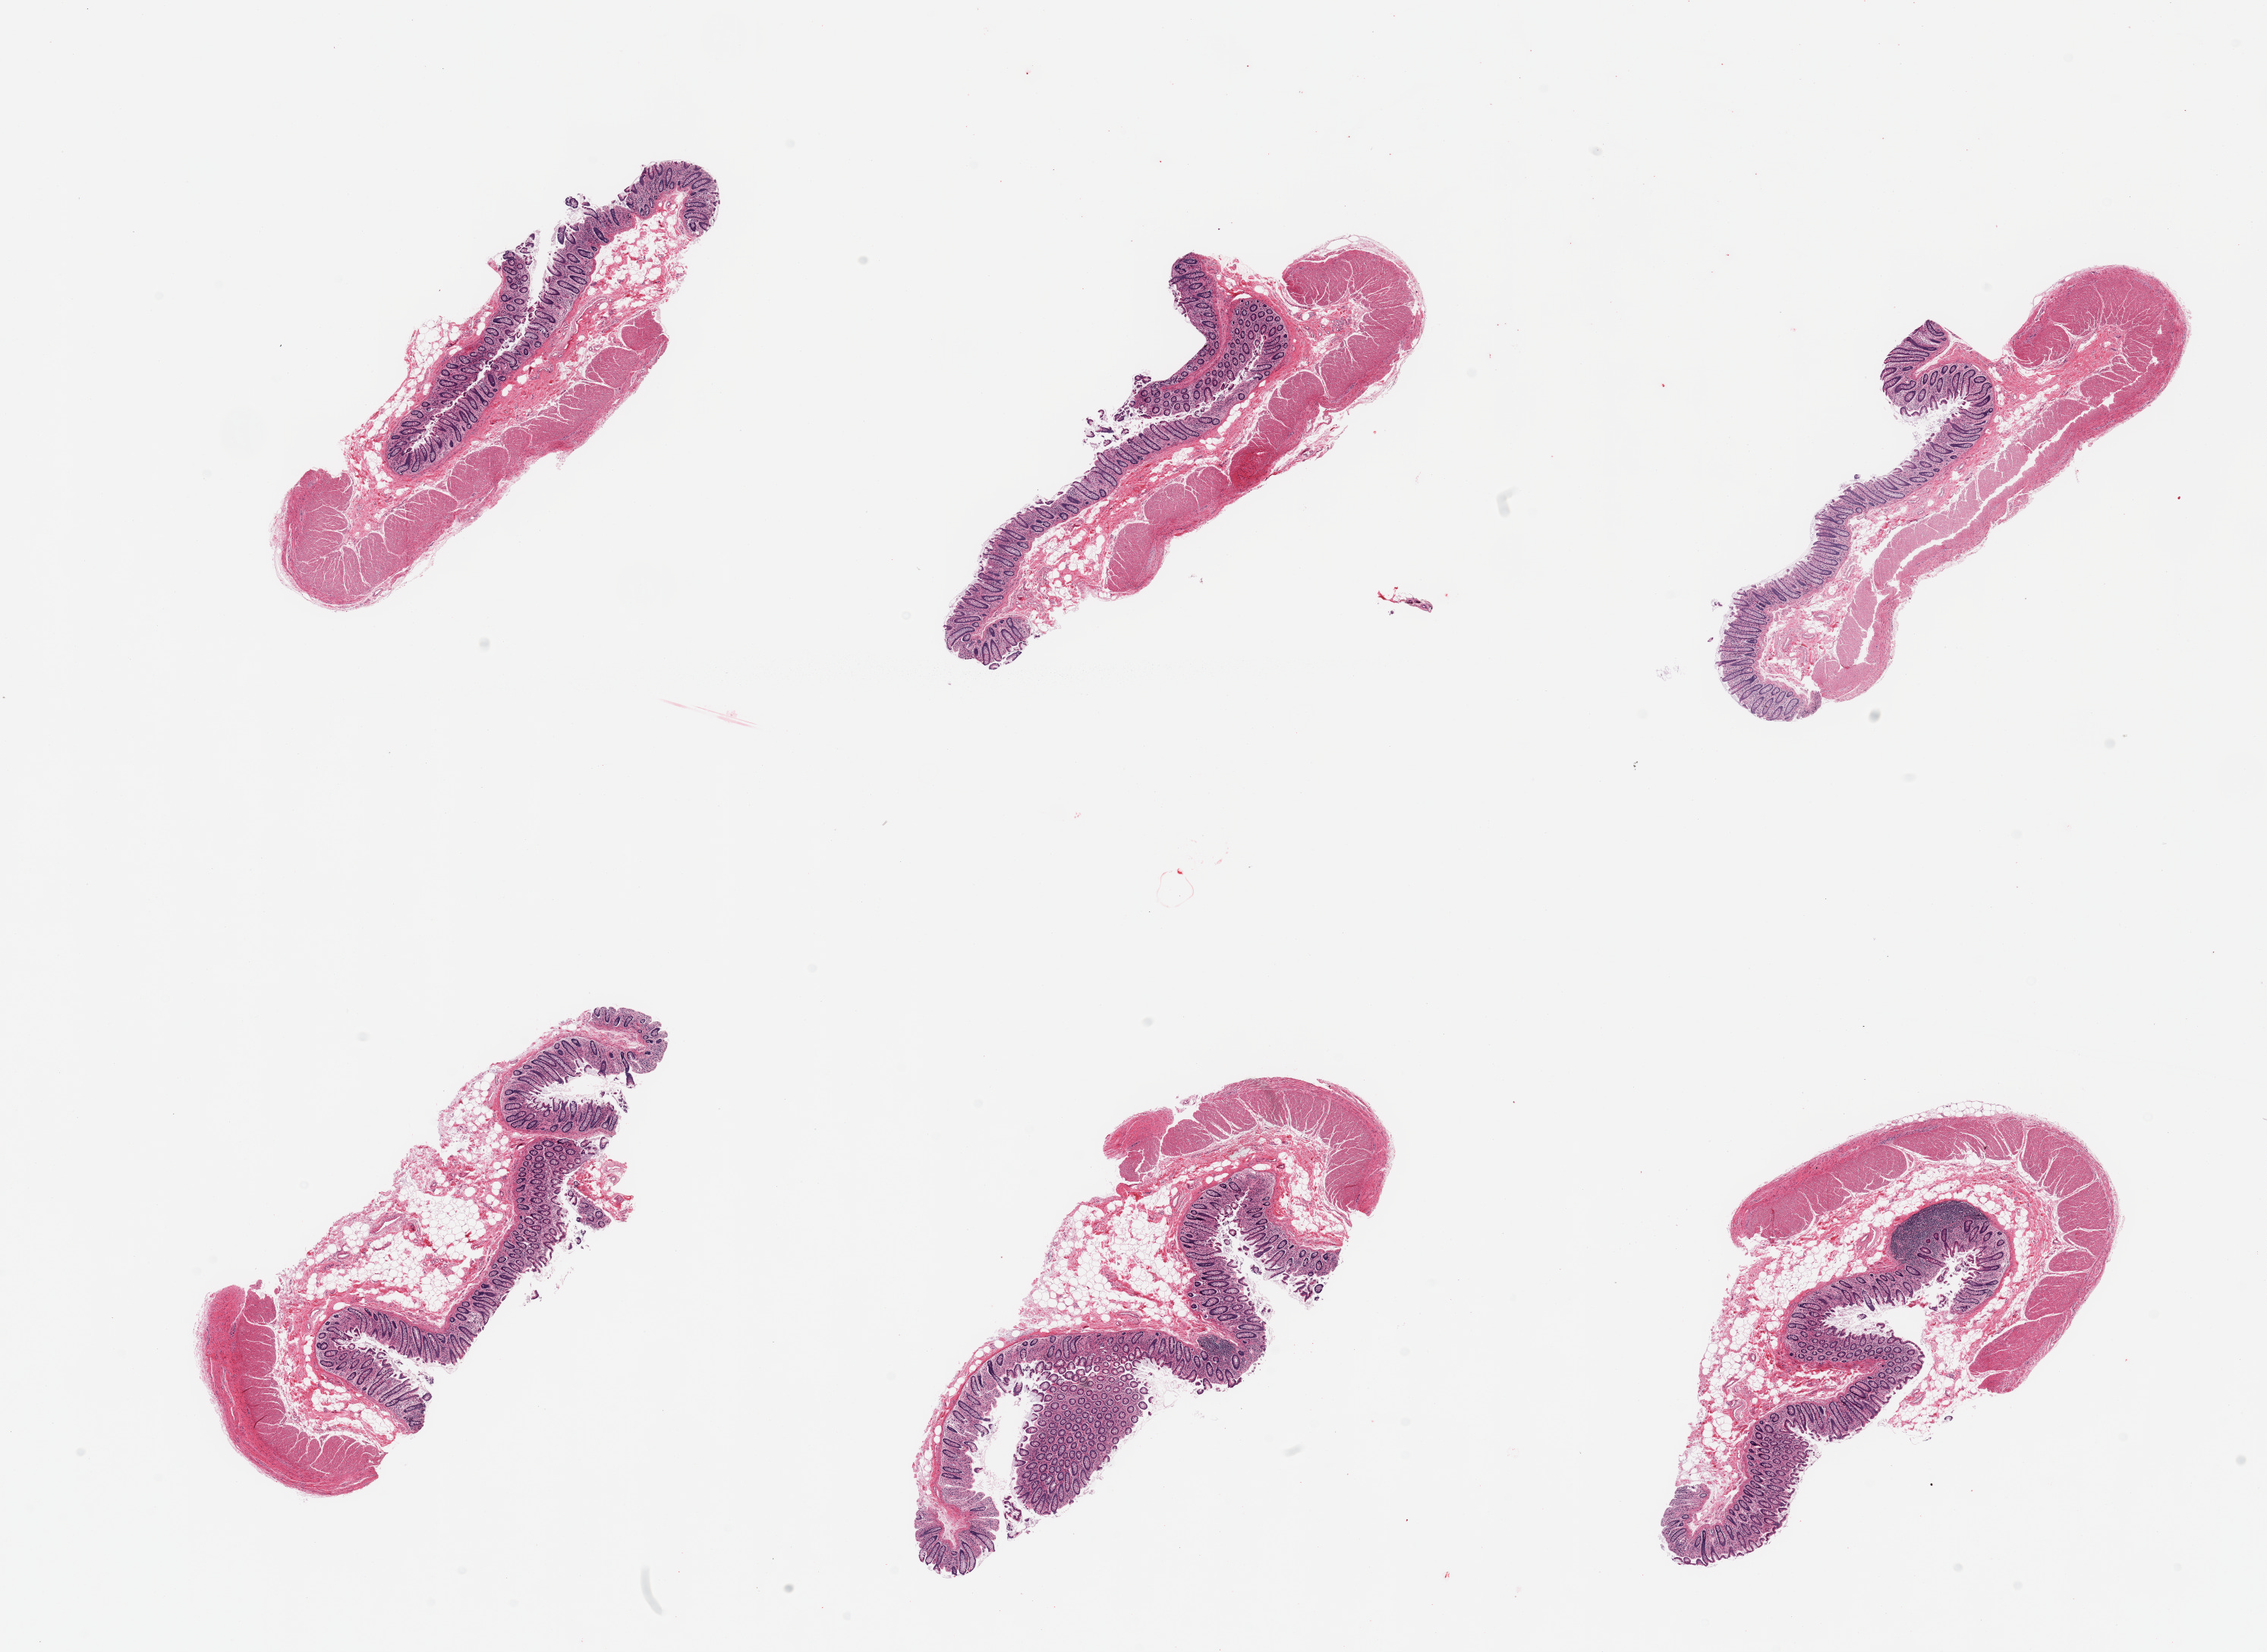
Whole-slide image, haematoxylin and eosin stain, brightfield, whole scanned area (about 23.6 x 17.2 mm) shown as a low-resolution overview; PAXgene-fixed, paraffin-embedded tissue; sampled site (target tissue): transverse colon; donor tissue sample. Male donor.
- reviewer comment on this tissue sample: 6 pieces; muscle in better shape than mucosa